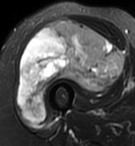
MRI of an extremity soft-tissue mass, one axial slice. Slice 47 of 95 in the series (ordered by position). T2-weighted fat-saturated. MR volume resampled by the dataset authors to the PET/CT grid (not the native acquisition matrix). 3.27 mm slice thickness. 135 × 146 image matrix, field of view 132 × 143 mm. Female patient. From the clinical record (not read from this slice): histological type: pleiomorphic undifferentiated sarcoma; grade: high; site of the primary tumour: right quadricep.
Annotated regions visible in this slice (expert contour drawn on MRI and transferred to this co-registered scan by the dataset authors):
- gross tumour volume including surrounding oedema: bounding box <19,20,123,122> (left, top, right, bottom; pixels)
- gross tumour volume (mass): <19,20,123,122>